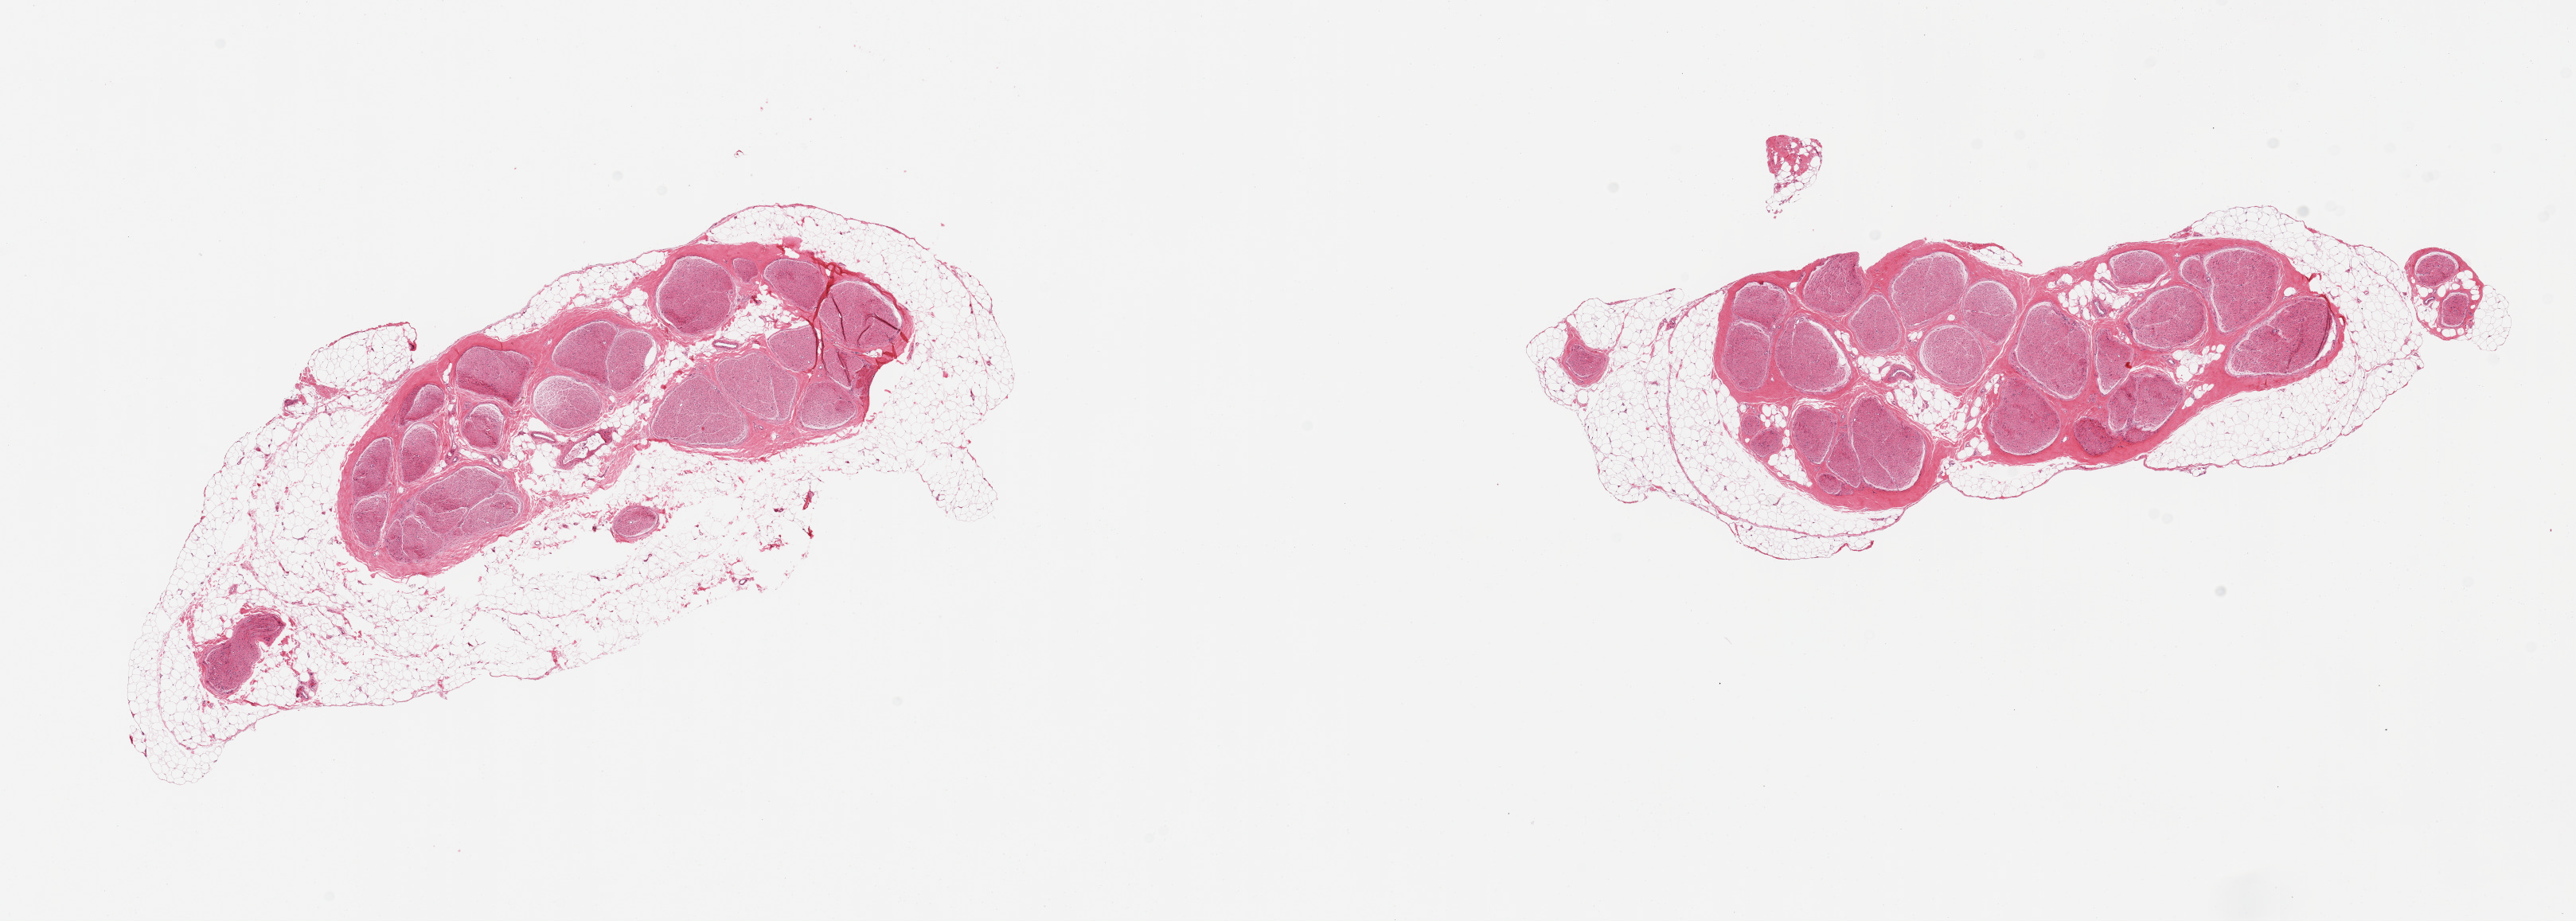
Digitized haematoxylin and eosin-stained section — low-resolution overview of the scanned area, about 25.6 x 9.2 mm; PAXgene-fixed paraffin-embedded (PFPE) section; target tissue: tibial nerve; tissue donor sample. Donor sex: male.
Pathologist's review note for this sample: 2 pieces; abundant extraneous fat (40 and 60%).